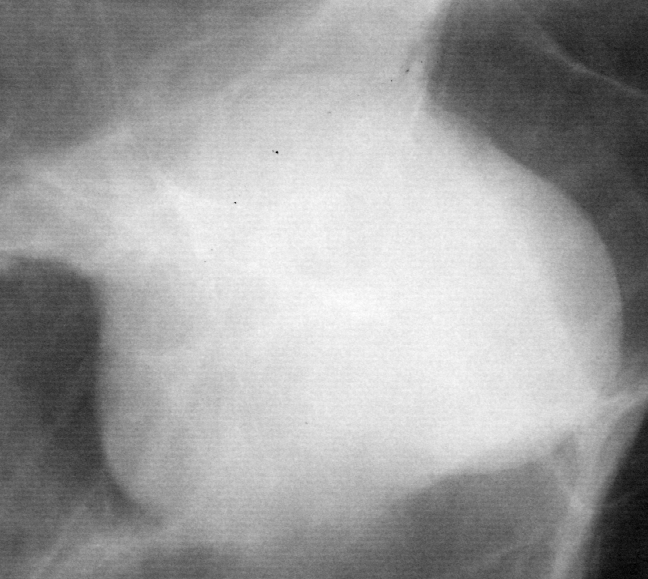
Crop from a digitized film mammogram around one marked abnormality, left breast, CC view.
Marked abnormality: mass, shape oval, margins circumscribed; BI-RADS assessment category 4; subtlety rating 5 on a 1 (subtle) to 5 (obvious) scale; pathology (as recorded): benign.